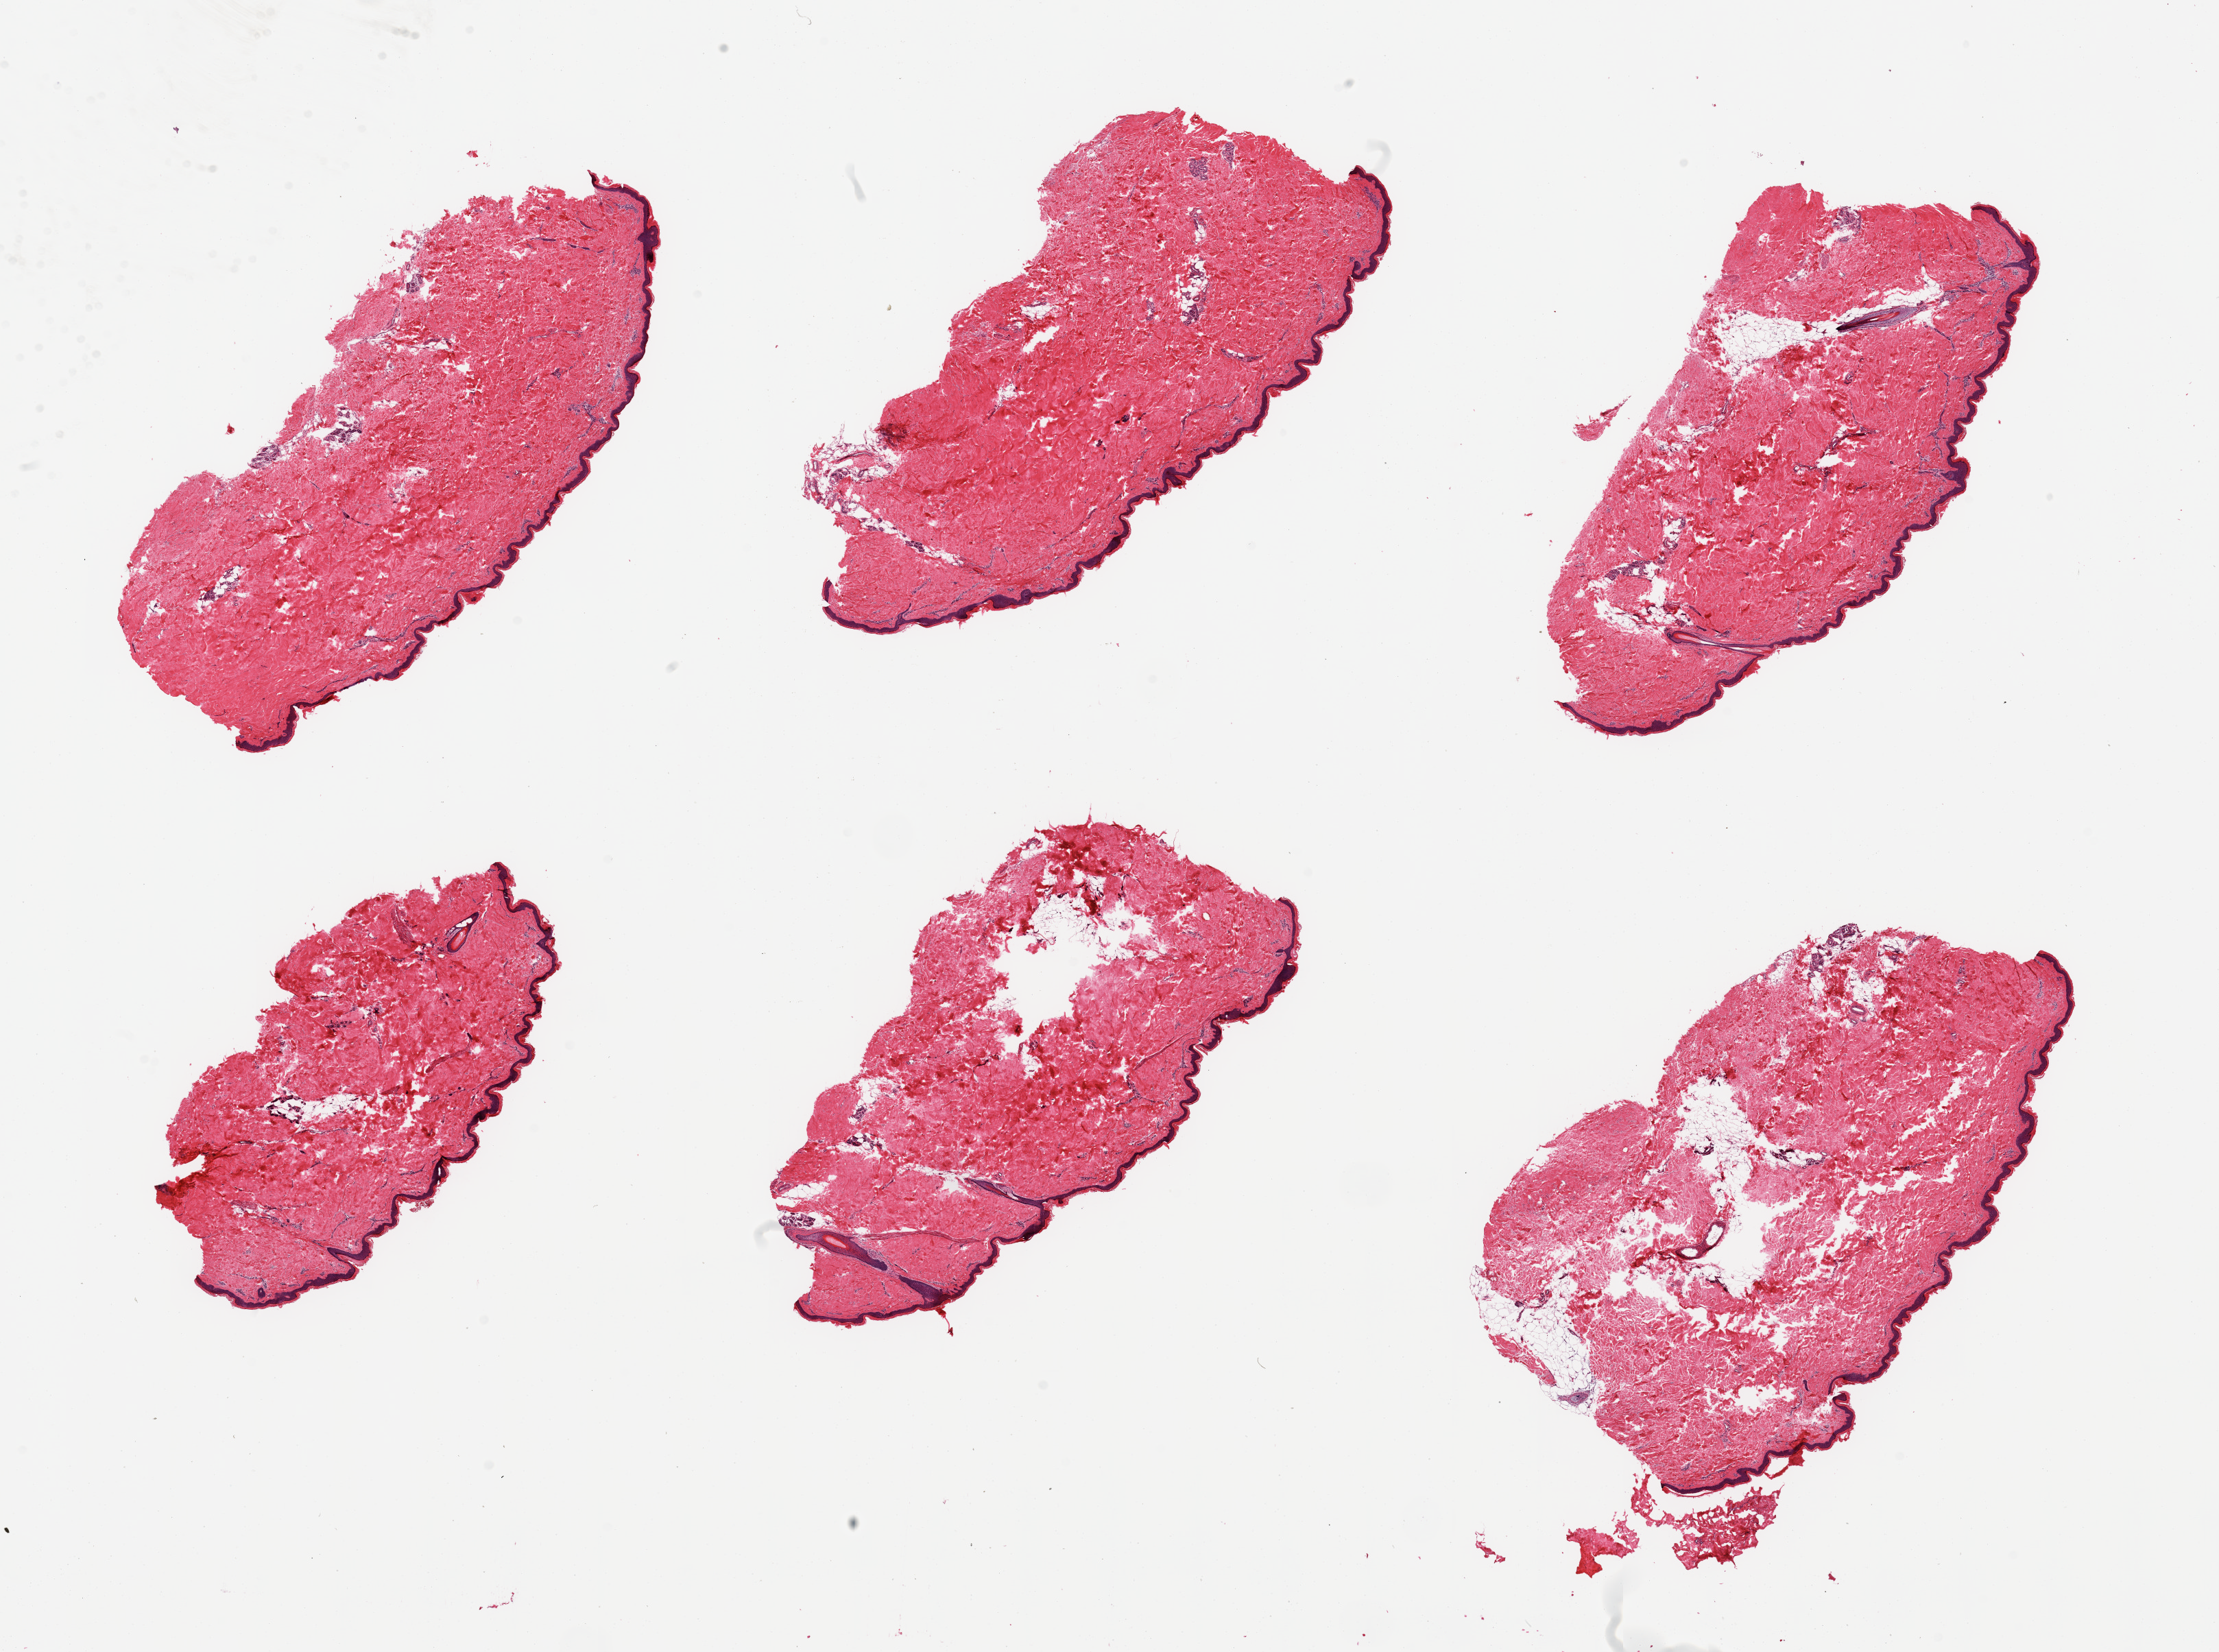
H&E whole-slide image — whole scanned area (about 25.6 x 19.1 mm, from a 20x scan) shown as a low-resolution overview, PAXgene-fixed paraffin-embedded (PFPE) section, sampled site (target tissue): skin of lower leg, donor tissue sample. Donor sex: male.
* pathologist's review note for this sample: 6 pieces, minimal dermal fat; squamous epithelium is ~50 microns